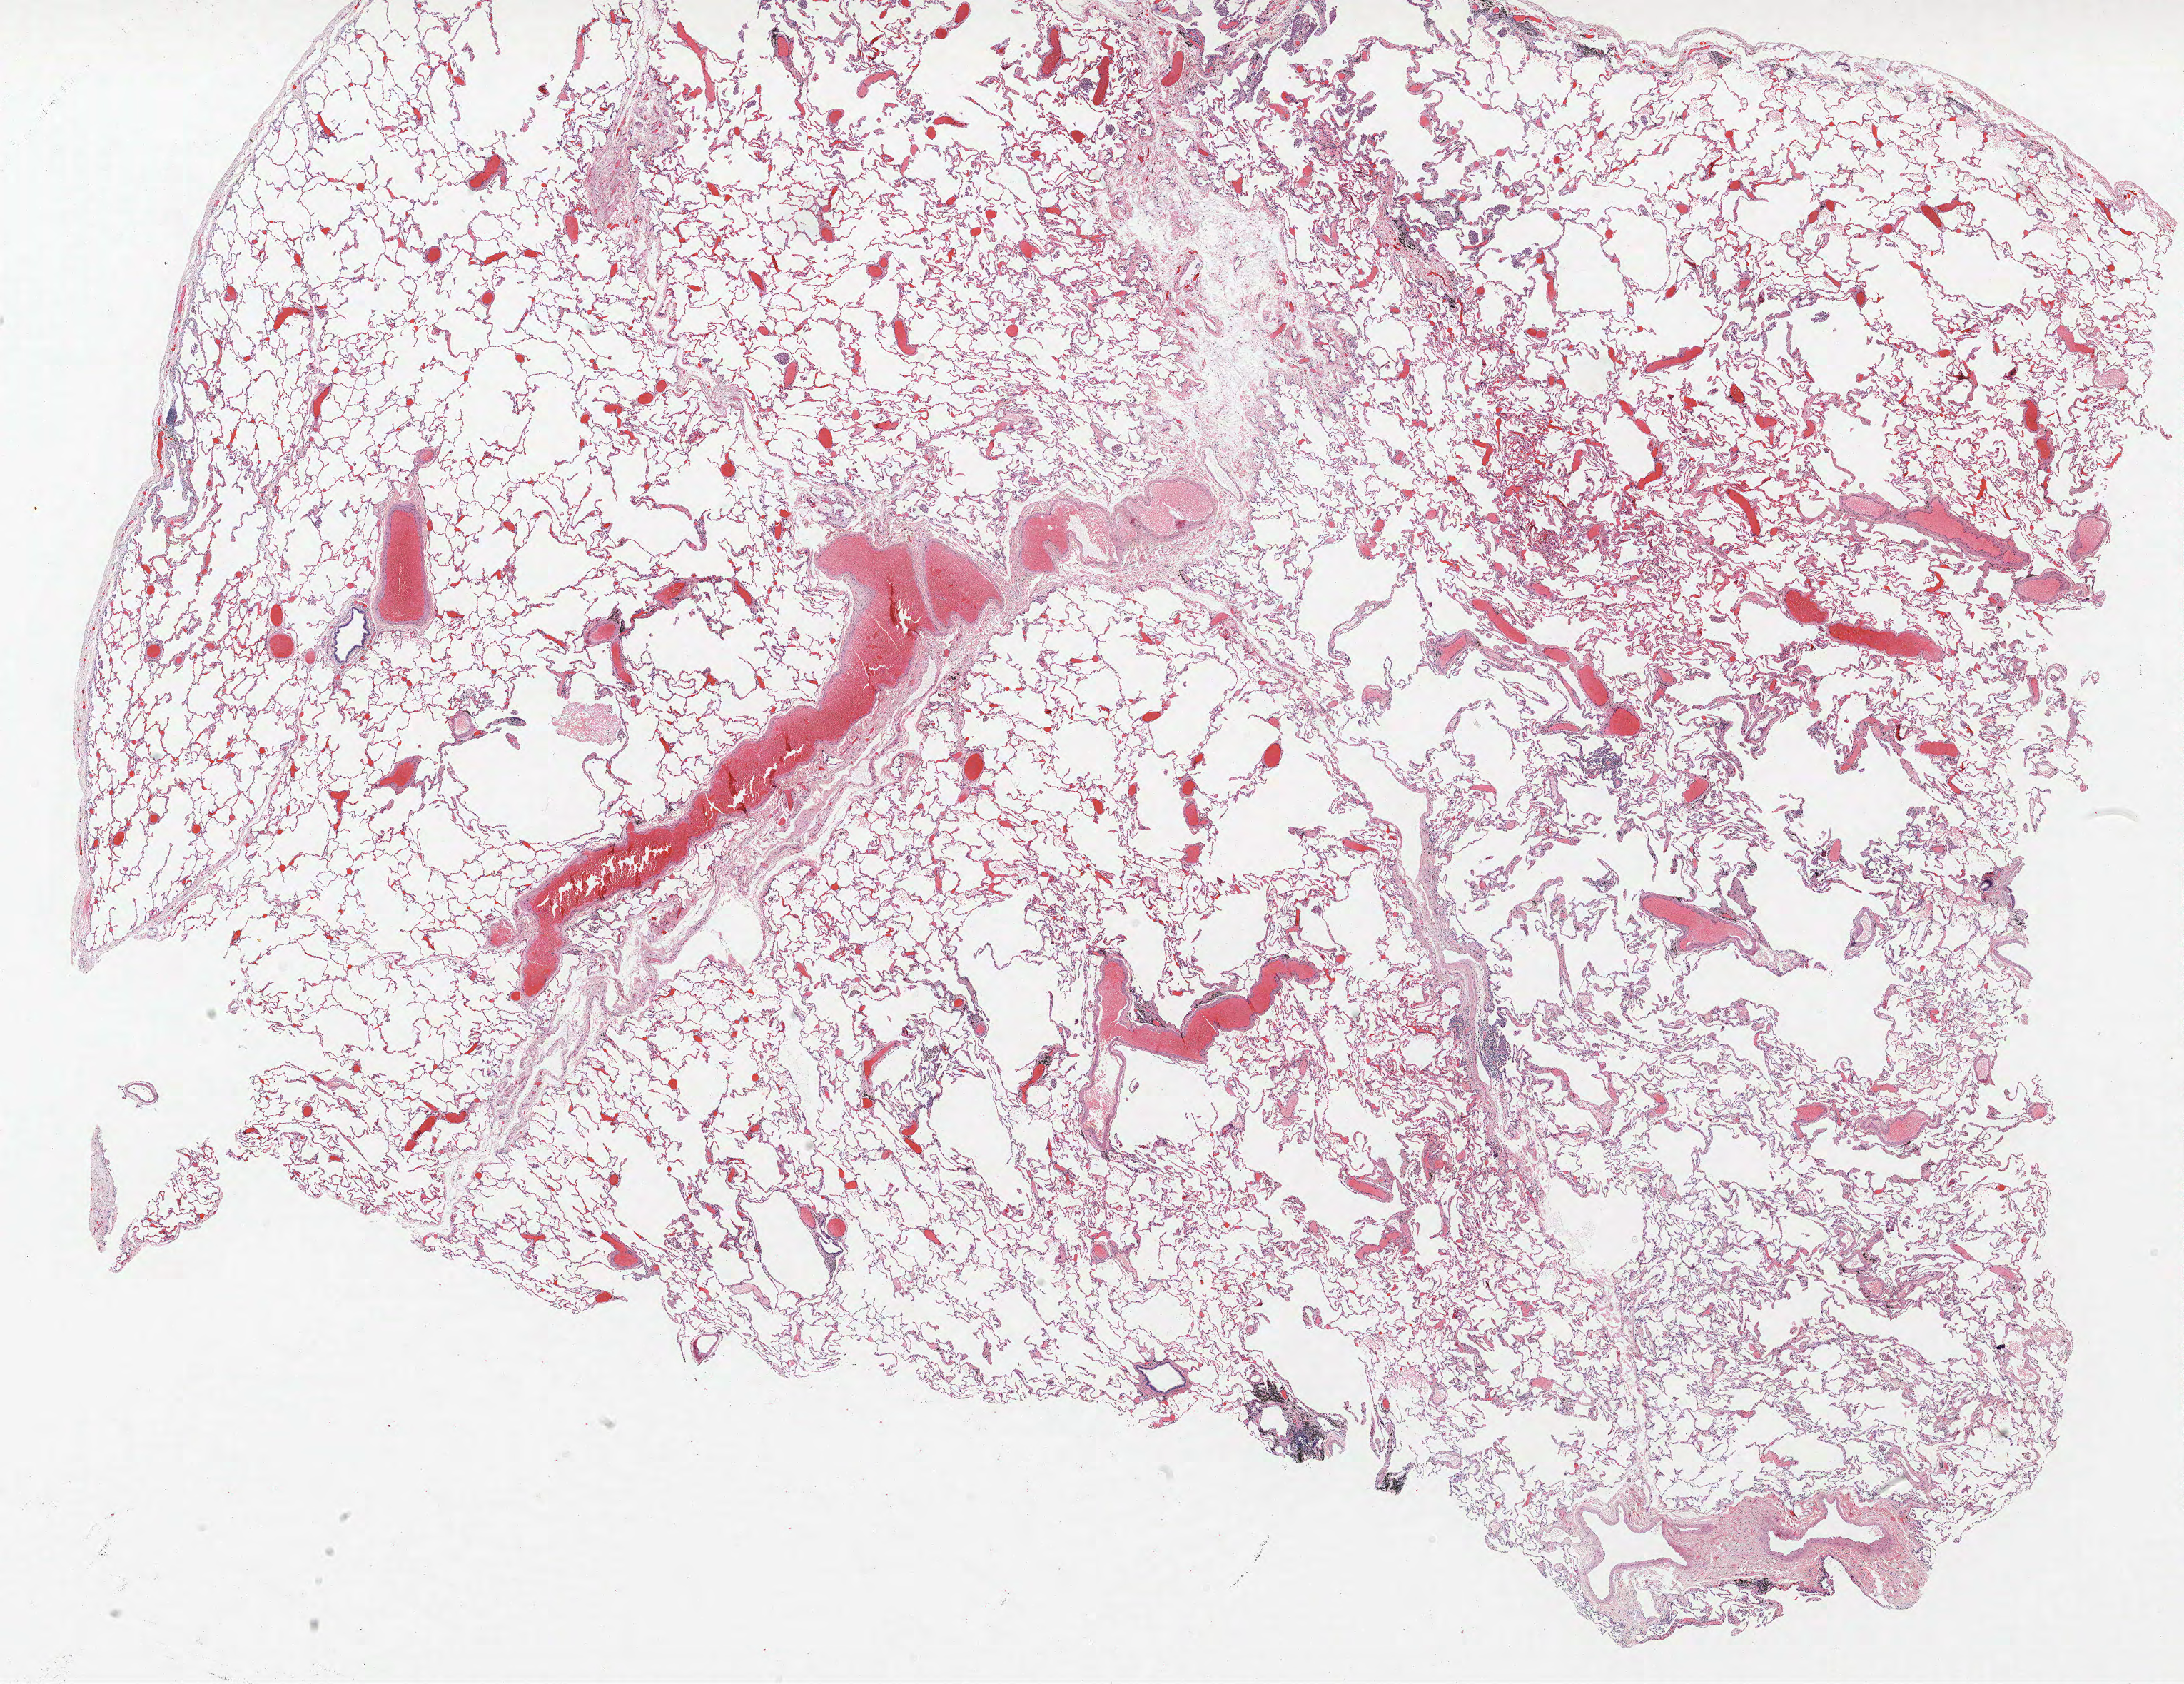
Hematoxylin and eosin (H&E) stained whole-slide image, whole scanned area (about 24.5 x 18.9 mm, acquisition: 40x scan) shown as a low-resolution overview. Formalin-fixed paraffin-embedded (FFPE) section. Lung. Male patient, aged 67 at enrolment. Former smoker at enrolment. Grade: poorly differentiated (G3).
Tumour size (pathology): 27 mm. Participant's lung-cancer diagnosis: Squamous cell carcinoma, NOS. Stage (AJCC 6th edition): IA. Primary tumour location (clinical record): right upper lobe. Note: participant had 2 primary lung cancers recorded; fields above describe the first.